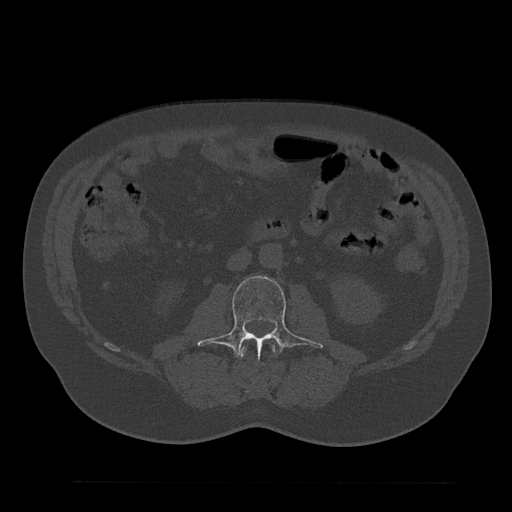
CT including the spine, one axial slice; position 44 of 797 along the scan axis; reconstruction kernel Br40s/3; bone window (W 1800 / L 400 HU); 0.5 mm slice thickness; 512 × 512 image matrix, field of view 430 × 430 mm. Male patient, age 61 years. From the clinical record (not read from this slice): primary cancer: prostate.
Structures marked on this image (semi-automatic segmentation, software-assisted and operator-edited):
- L2 vertebra: bounding box (x1, y1, x2, y2) in pixels: (240, 344, 276, 358)
- L3 vertebra: (198, 276, 323, 358)